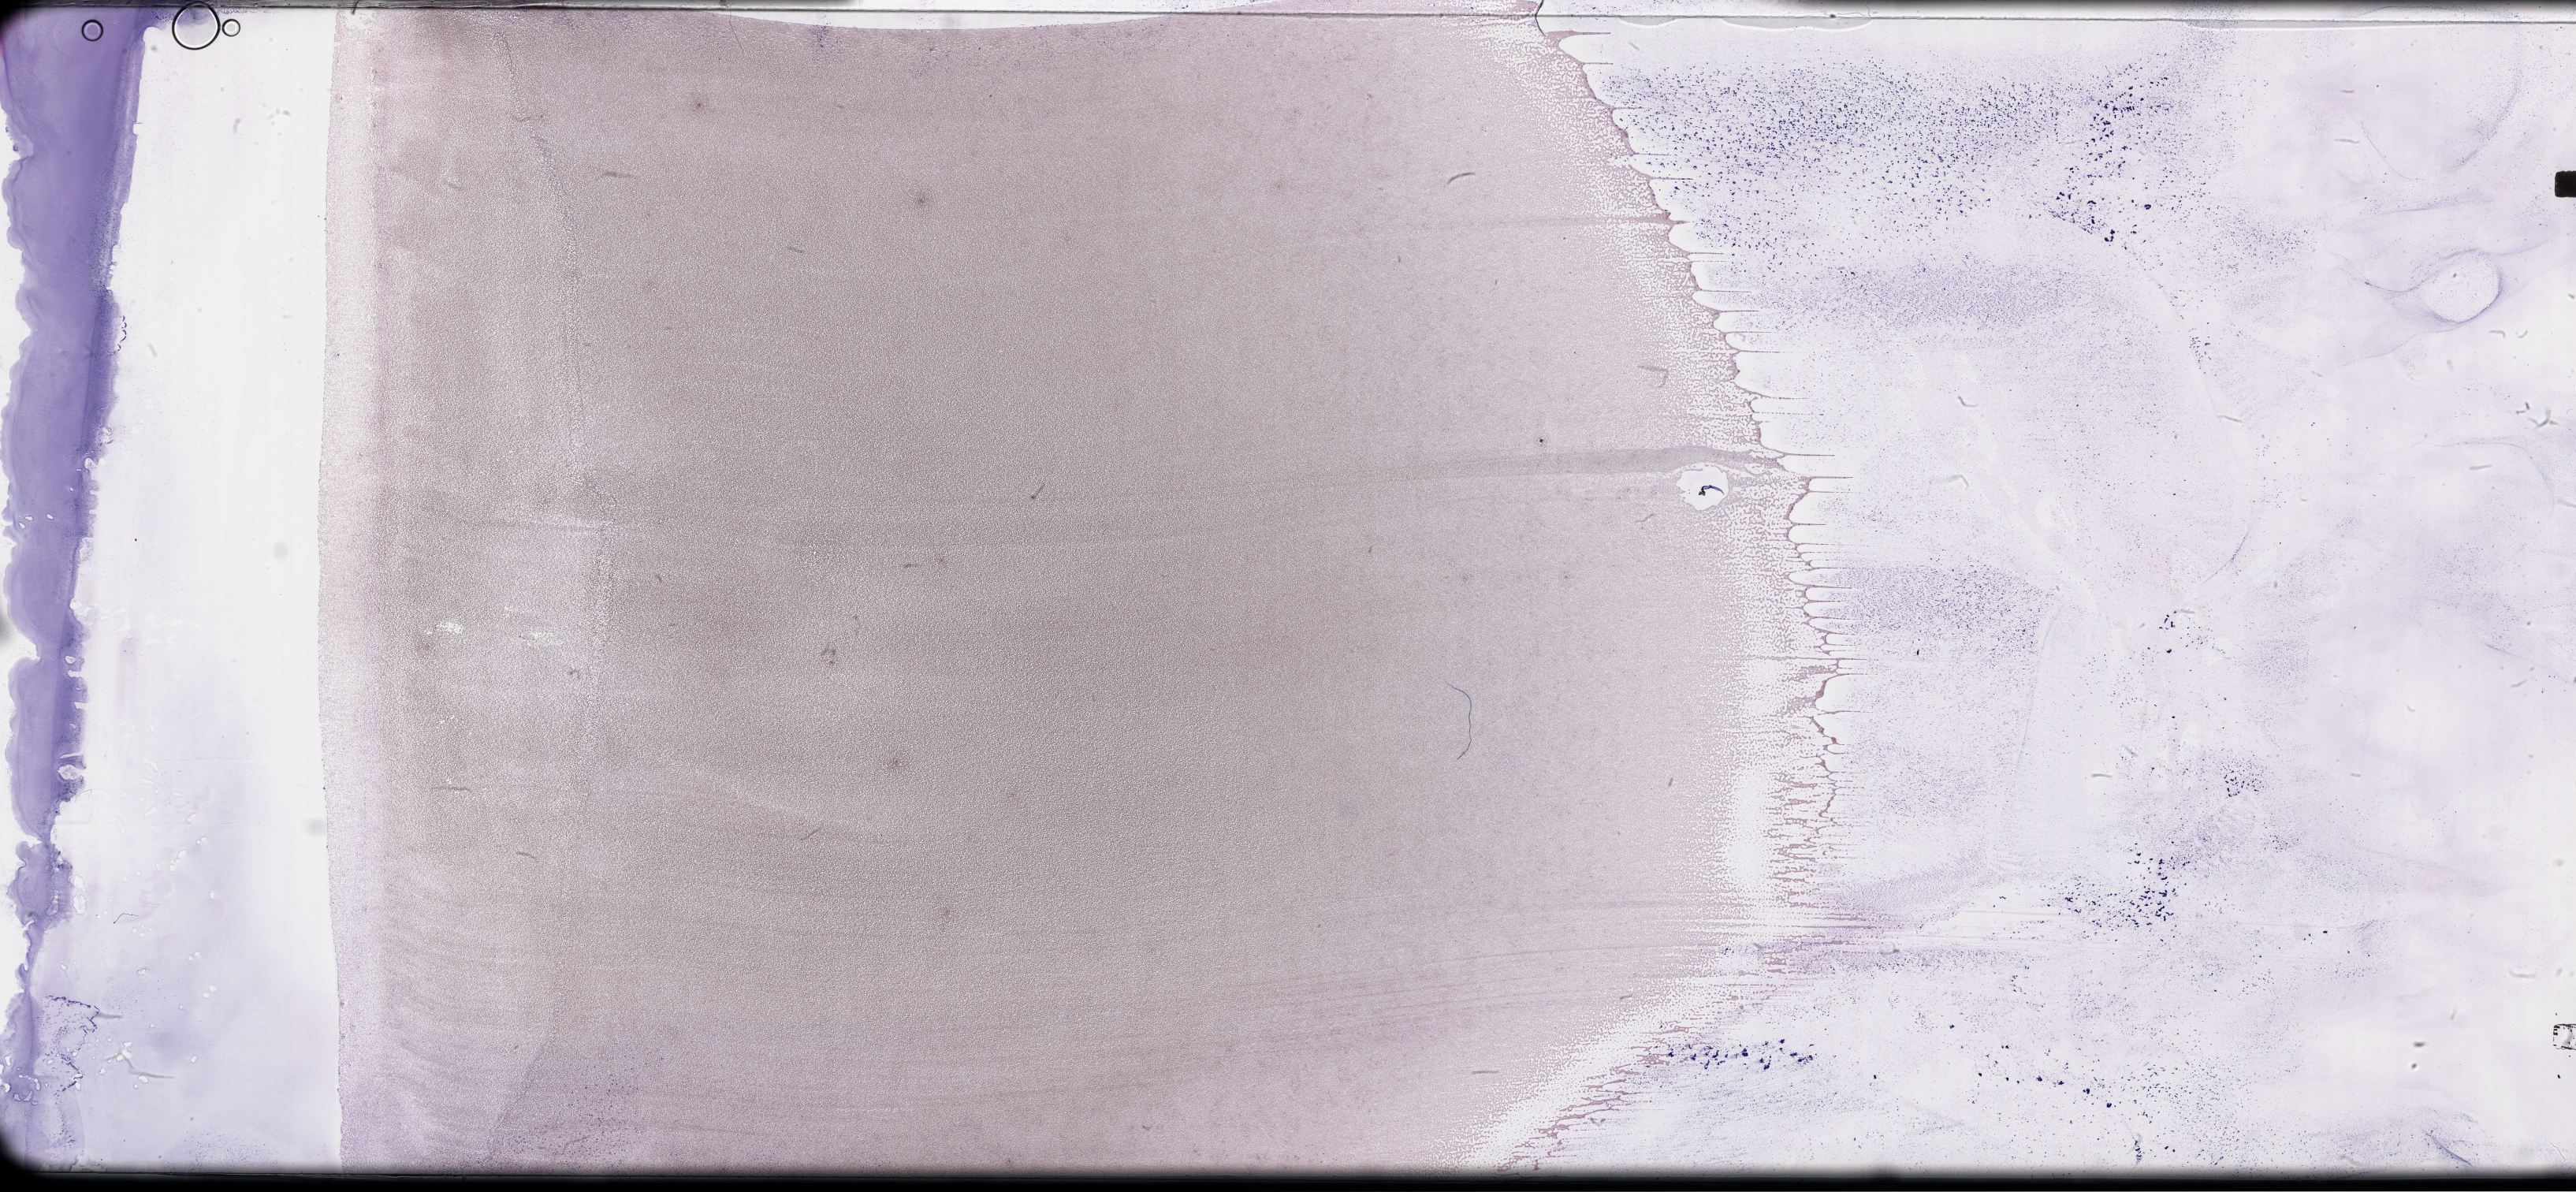
Wright-Giemsa-stained whole blood smear, whole-slide image — whole scanned area (about 52.8 x 24.4 mm) shown as a low-resolution overview. Patient sex: male.
From a patient with: Plasma Cell Myeloma.